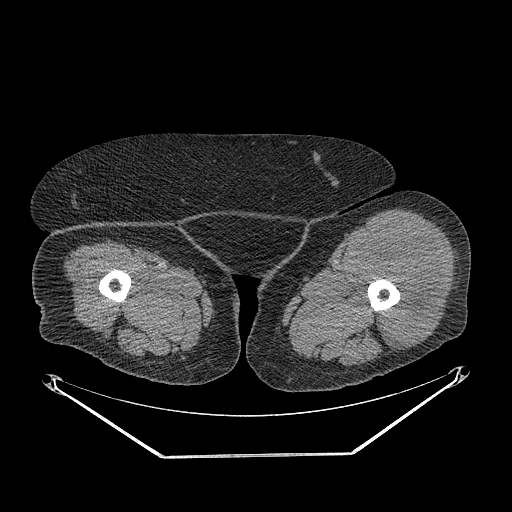
CT of an extremity soft-tissue mass (from a PET/CT study), one axial slice. Position 242 of 267 along the scan axis. Reconstruction kernel STANDARD. Soft-tissue window (W 400 / L 40 HU). 3.75 mm slice thickness. 512 × 512 image matrix. Female patient. Case-level facts recorded for this patient, not image findings: histological type: undifferentiated – high grade; grade: high; site of the primary tumour: left thigh.
Outlined on this slice (expert contour drawn on MRI and transferred to this co-registered scan by the dataset authors):
- gross tumour volume including surrounding oedema: bounding box [x1, y1, x2, y2] px = [352, 231, 441, 350]
- gross tumour volume (mass): [354, 231, 439, 350]